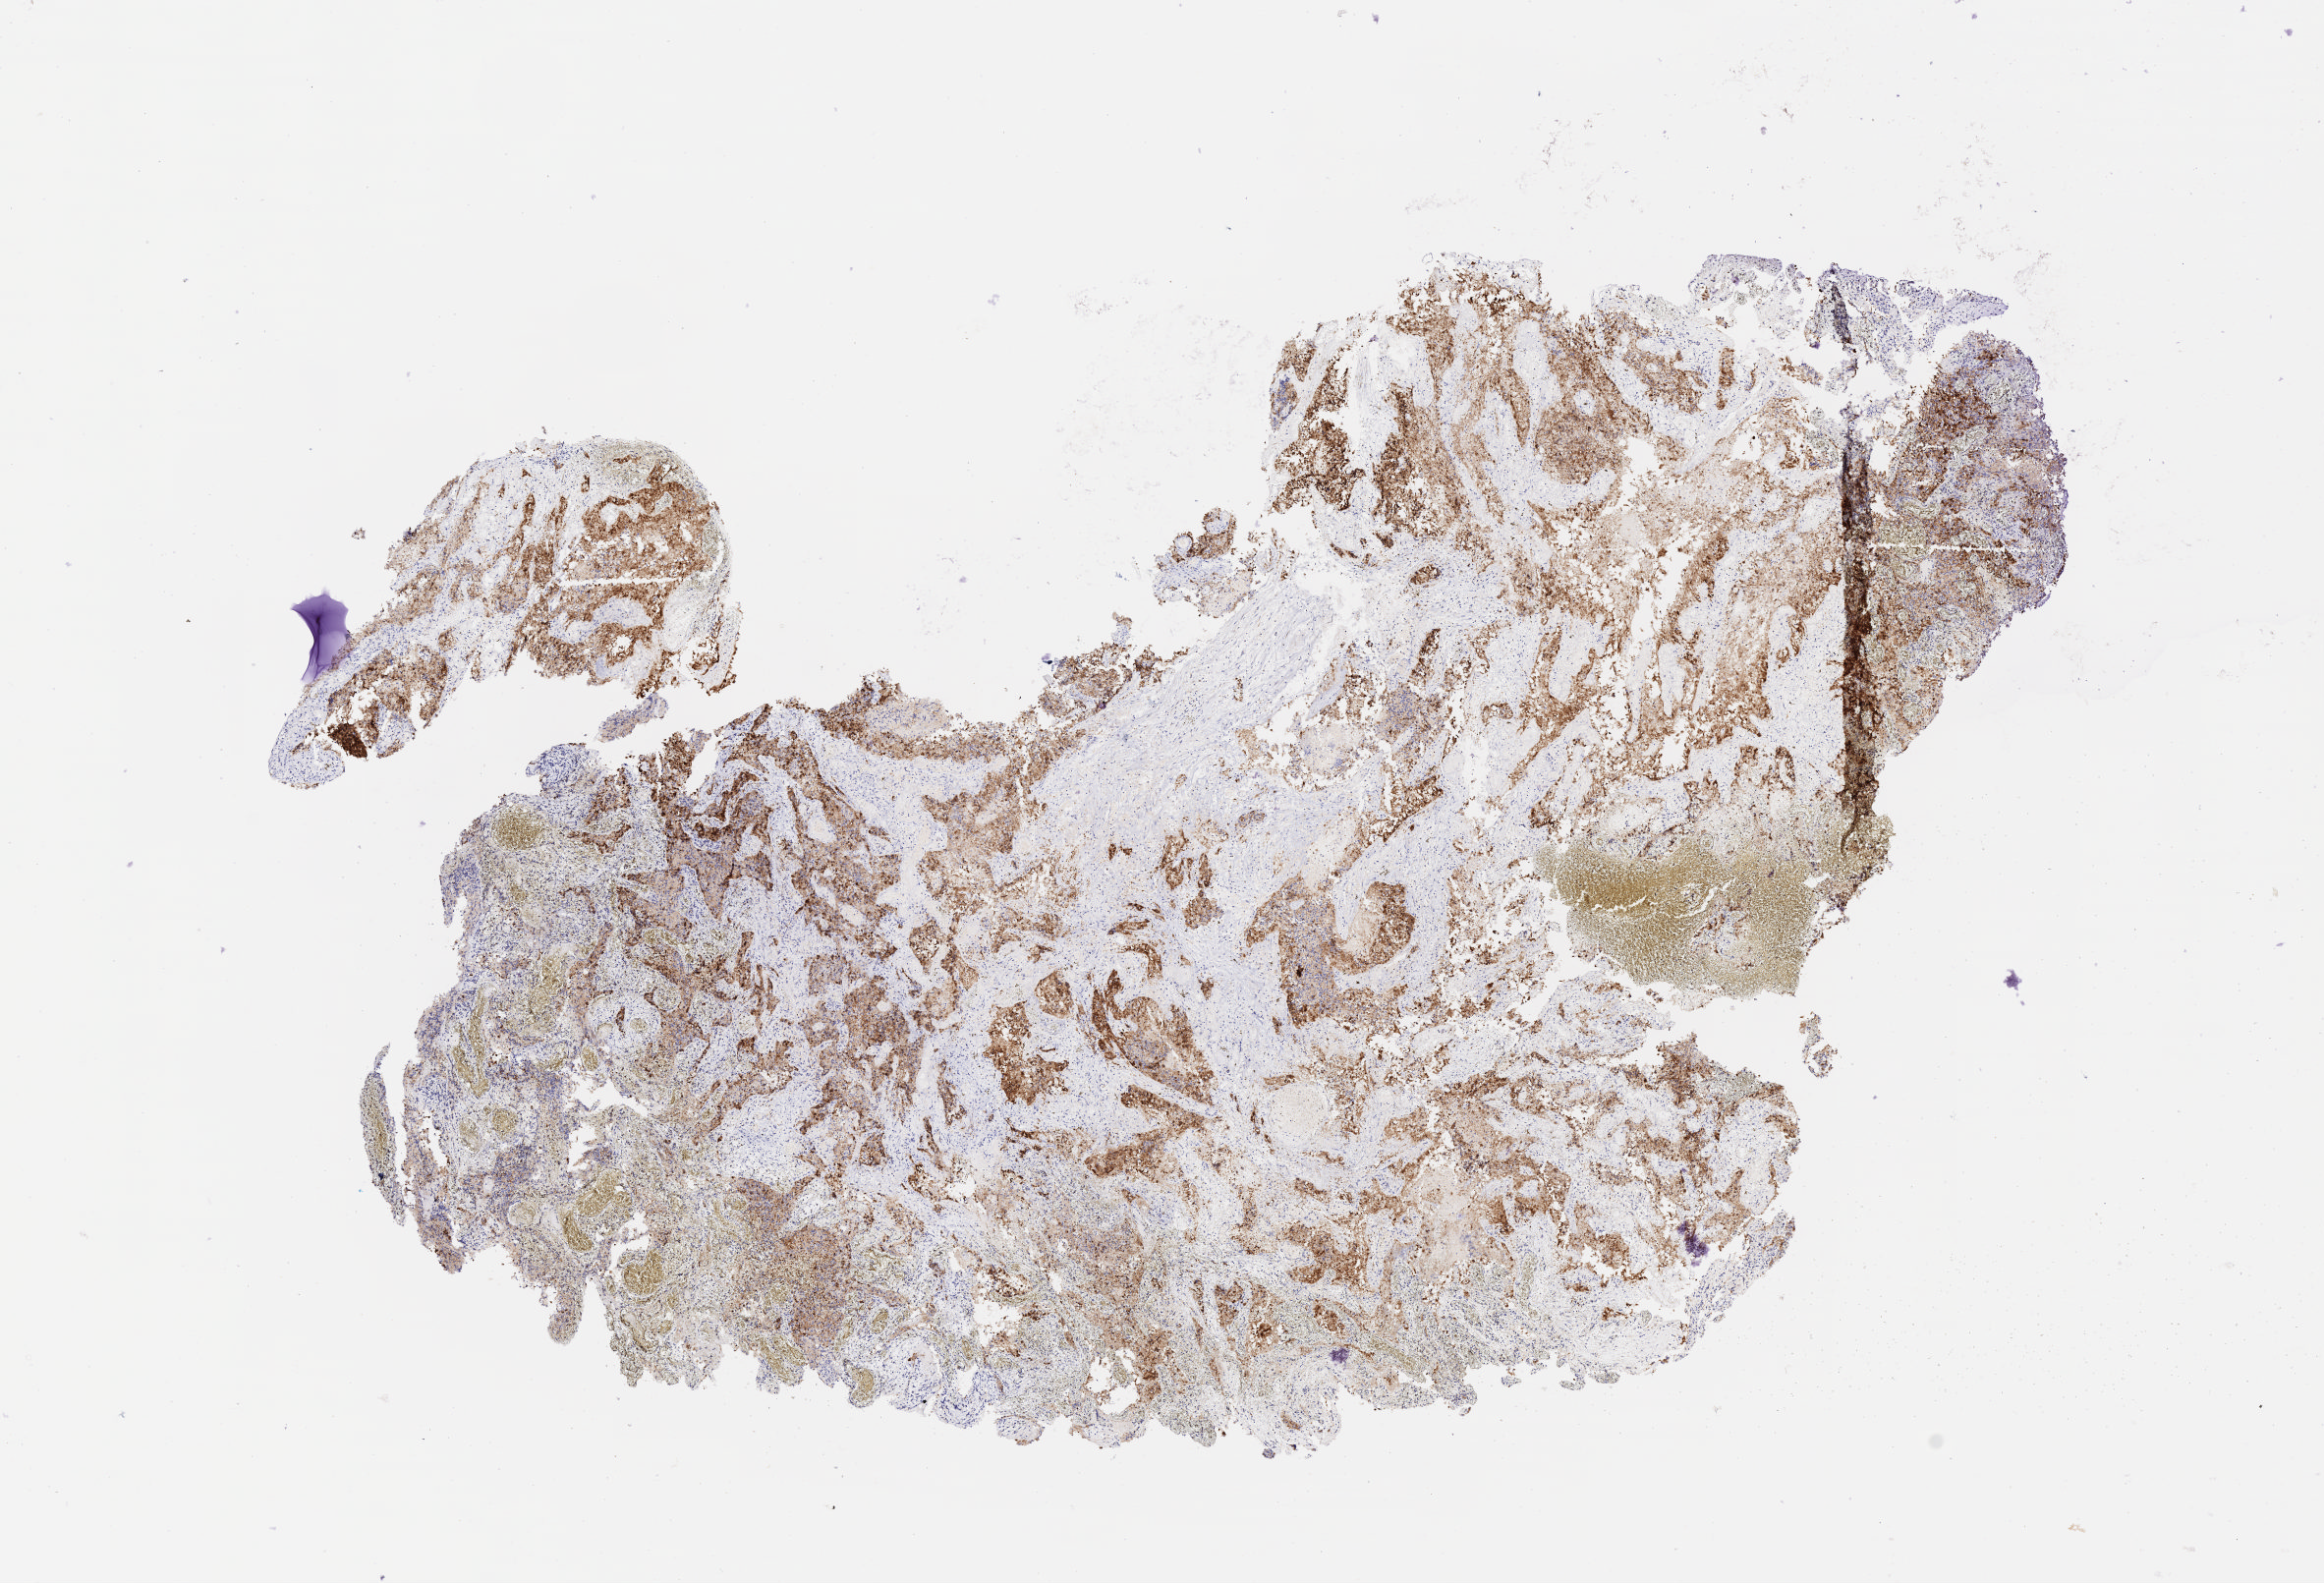
Immunohistochemistry (IHC) whole-slide image stained for p16 (p16INK4a), a low-resolution overview of the entire scanned area, about 9.6 x 6.5 mm, tumor tissue, anatomic site: cervix. Patient female; 51 years old.
Histologic diagnosis: Squamous cell carcinoma, keratinizing, NOS.